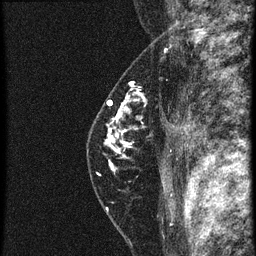
Breast MRI (dynamic contrast-enhanced), one sagittal slice. Slice 43 of 60 in the series (ordered by position). 4 images stored at this slice position (order not interpretable as contrast timing). 1.5 T. TE 4.2 ms, TR 20.4 ms. 256 × 256 image matrix. Female patient, age 46 years. Case-level facts recorded for this patient, not image findings: setting: breast cancer imaged before/during neoadjuvant chemotherapy; receptor status: triple-negative.
Outlined on this slice (semi-automatic segmentation, software-assisted and operator-edited):
- analysis volume of interest (the breast-tissue region the enhancement analysis was run in; not a lesion): box from (x=88, y=82) to (x=181, y=185) px
- tumour enhancement mask (voxels above the 90 % enhancement threshold inside the analysis volume of interest): (x=106, y=82)–(x=141, y=171)